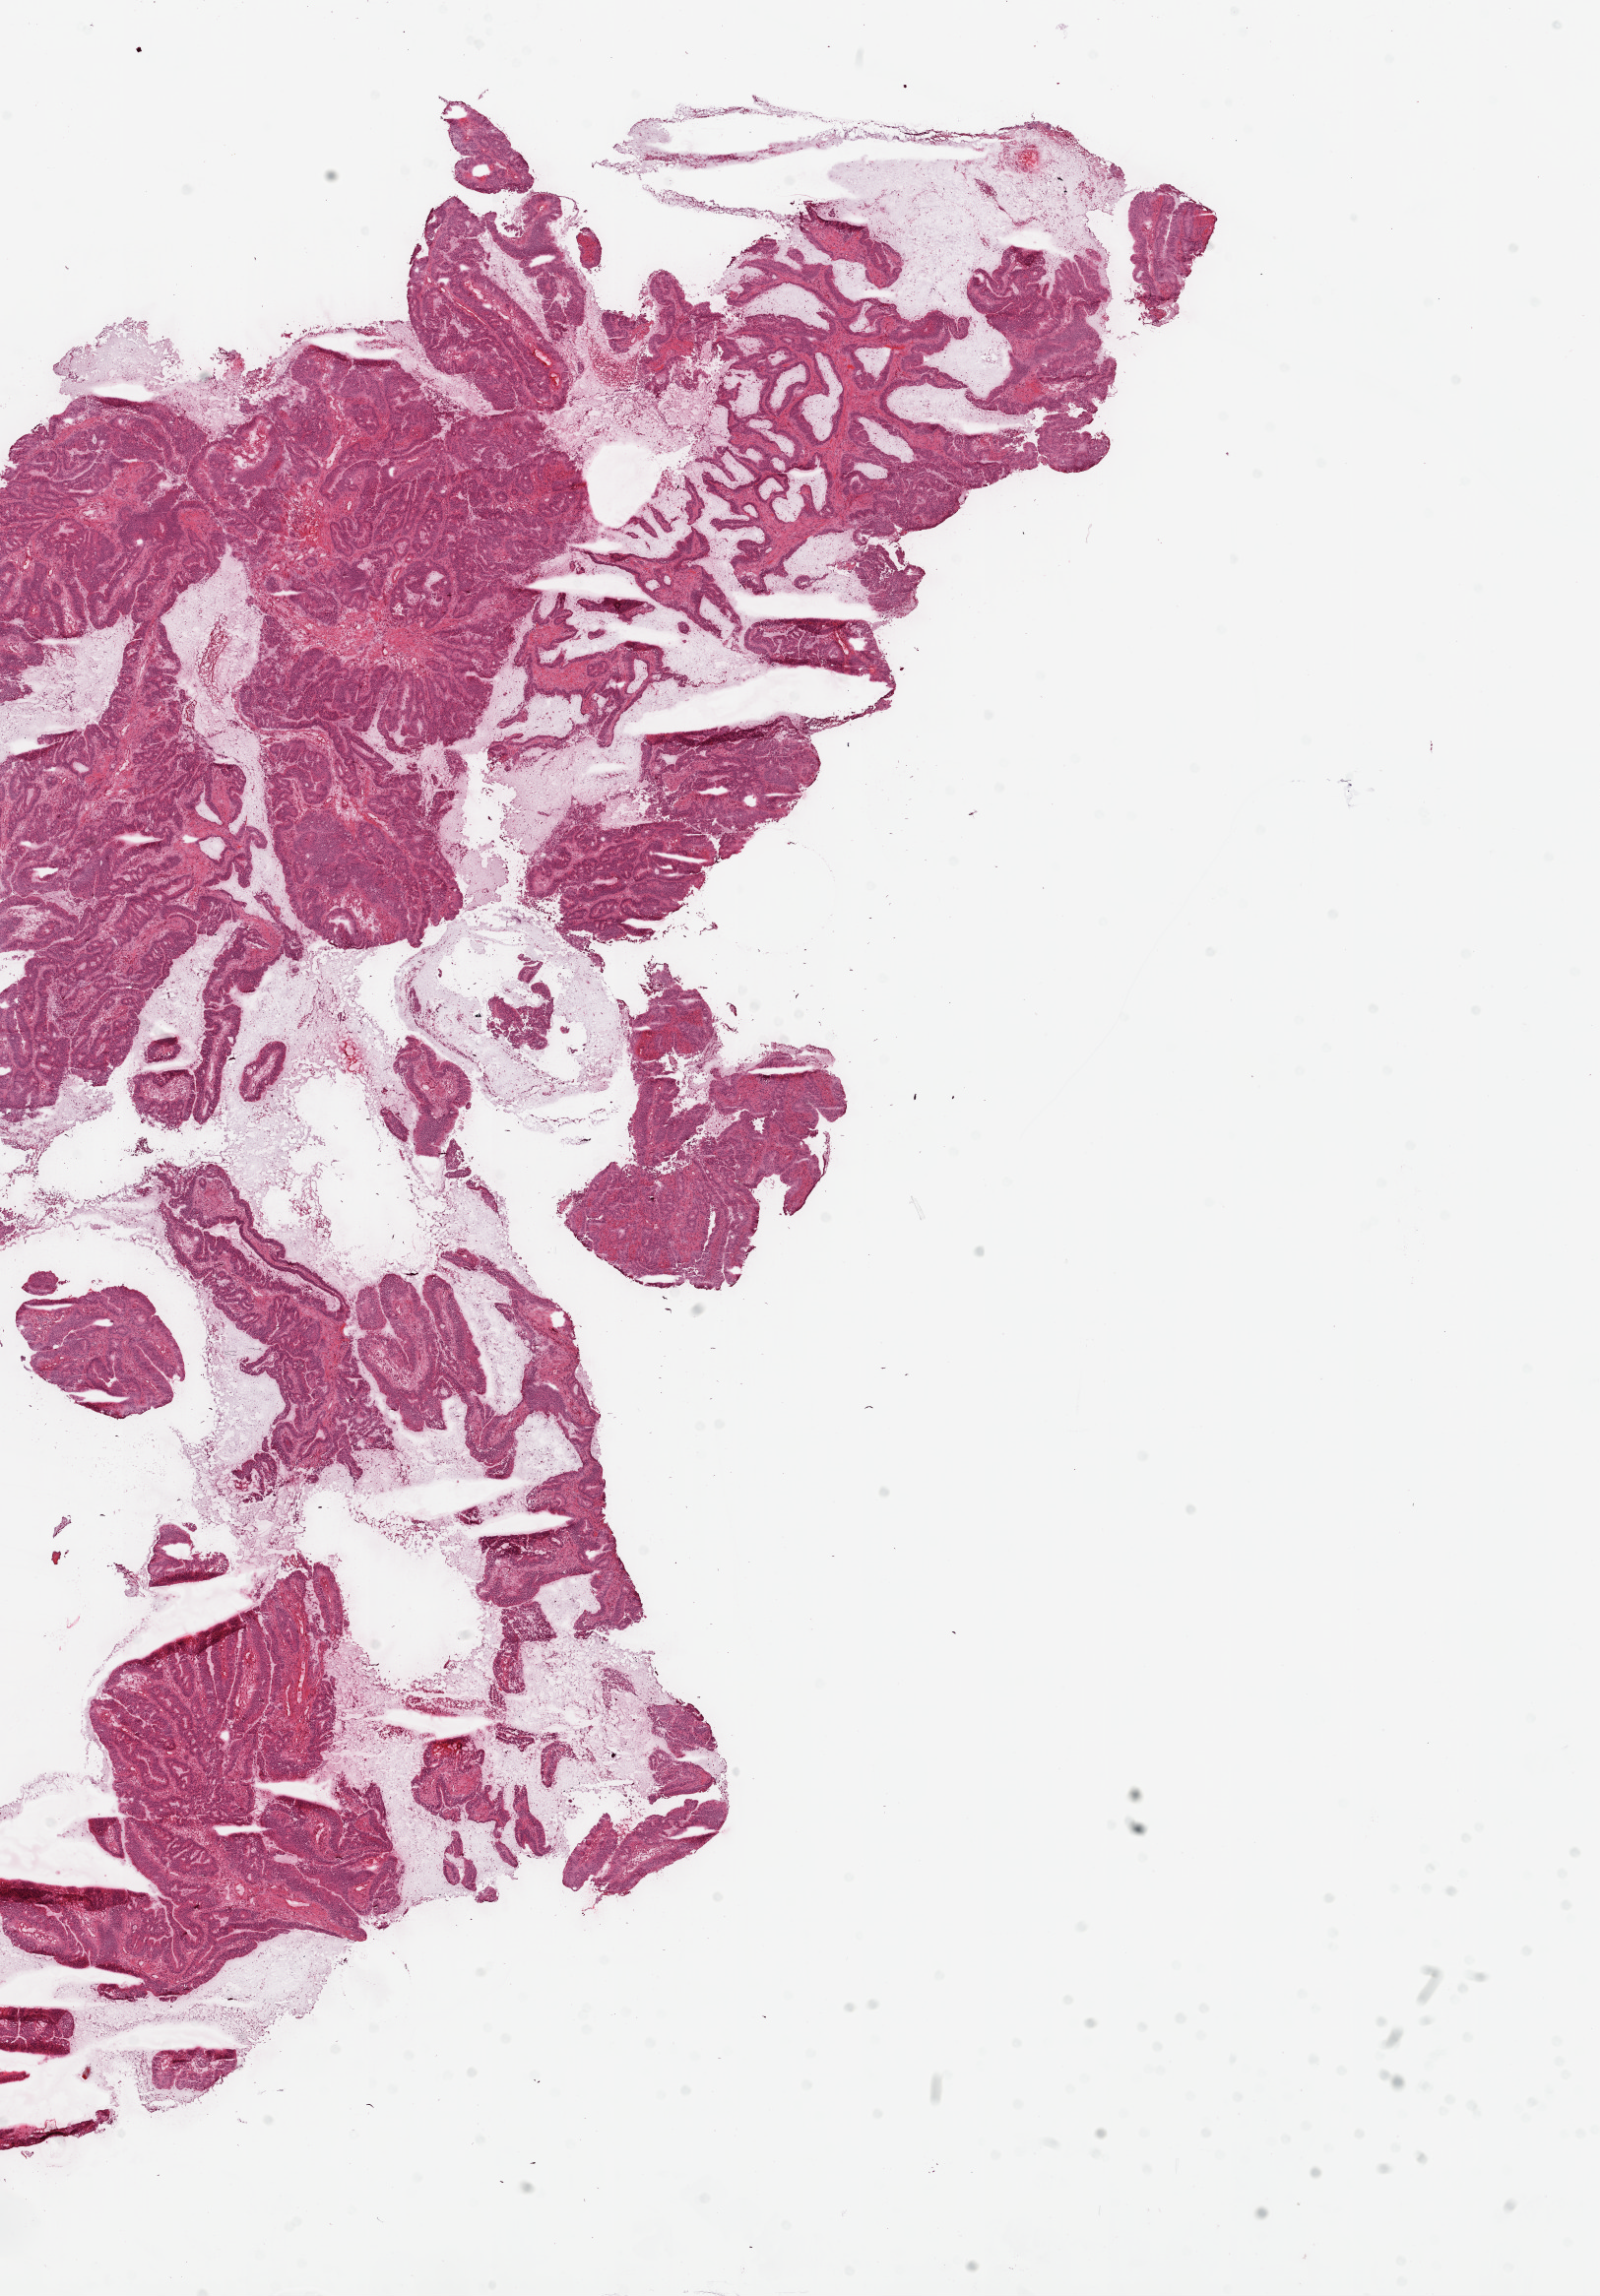
Digitized H&E-stained tissue section (whole slide) — low-resolution overview of the scanned area, about 13.0 x 18.7 mm (slide scanned at 20x), frozen section from the top of the tissue portion, primary tumour sample from the colon. Patient: male, age at initial diagnosis 61 years. Composition of this section per pathologist review: tumour cells 70%, tumour nuclei 80%, normal cells 15%, stromal cells 15%, necrosis 0%.
Pathologic diagnosis: Adenocarcinoma, NOS (sigmoid colon). AJCC pathologic stage: I. Lymph nodes positive (case pathology): 0 of 17 examined.